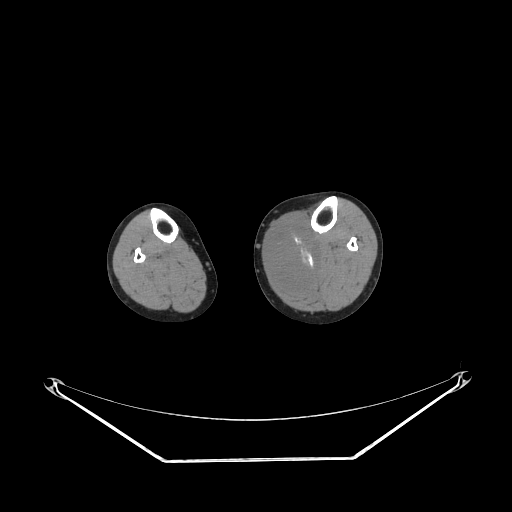
CT of an extremity soft-tissue mass (from a PET/CT study), one axial slice. Slice 139 of 223 in the series (ordered by position). Reconstruction kernel STANDARD. 140 kVp. Soft-tissue window (W 400 / L 40 HU). 512 × 512 image matrix, field of view 500 × 500 mm. Female patient. From the clinical record (not read from this slice): histological type: extraskeletal high grade osteogenic sarcoma; grade: high; site of the primary tumour: left calf.
Outlined on this slice (expert contour drawn on MRI and transferred to this co-registered scan by the dataset authors):
- gross tumour volume (mass): bounding box [x1, y1, x2, y2] px = [269, 226, 318, 287]